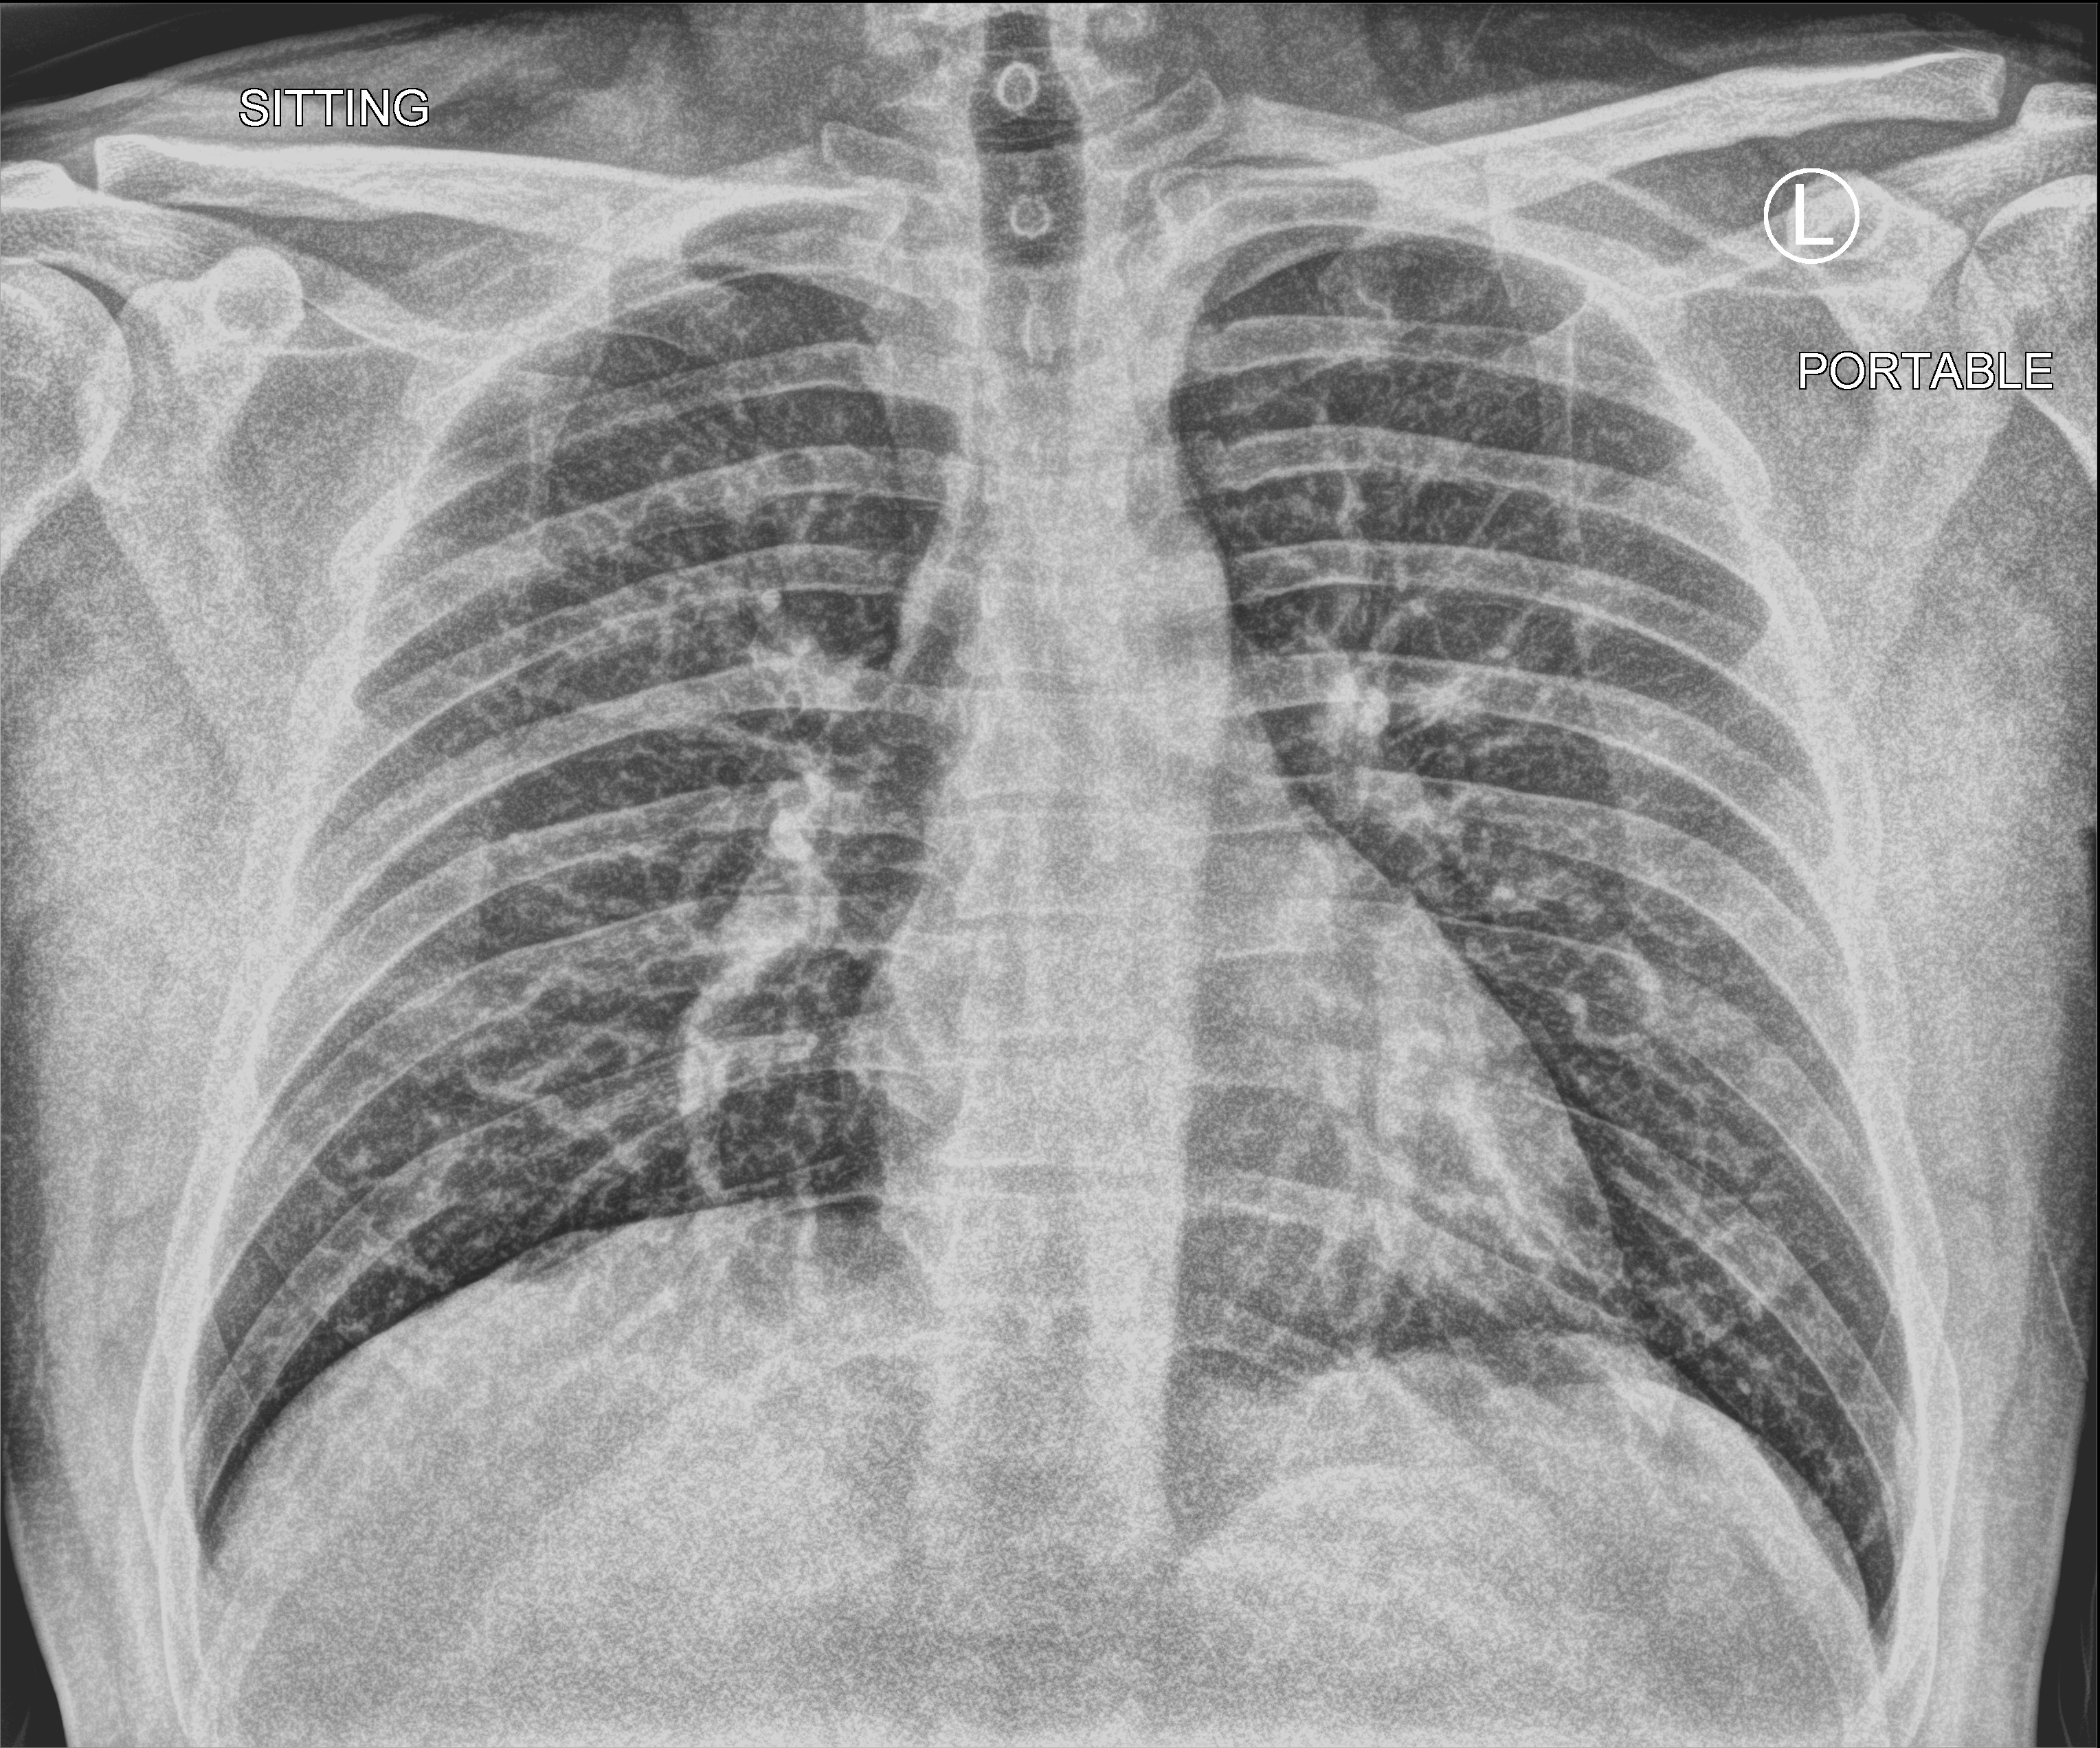
Chest X-ray (portable), anteroposterior (AP) projection. Patient hospitalised with COVID-19; male, aged 18–59 years.
Admission-level facts for this patient (not findings on this image; timing relative to this image not recorded):
- mechanically ventilated during this hospital stay: no
- hypertension (admission record): no